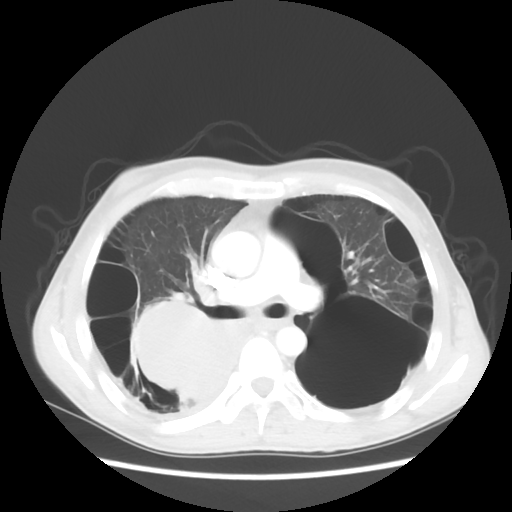
Chest CT, one axial slice. Reconstruction kernel STANDARD. Lung window (W 1500 / L -600 HU). 5 mm slice thickness. 512 × 512 image matrix, field of view 351 × 351 mm. Patient: male, 41 years. Case-level facts recorded for this patient, not image findings: clinical TNM (as recorded): T4 N0 M1a.
Structures marked on this image (rectangle marked by the reading radiologist):
- lung tumour (recorded histology: large cell carcinoma): bounding box <122,291,259,432> (left, top, right, bottom; pixels)